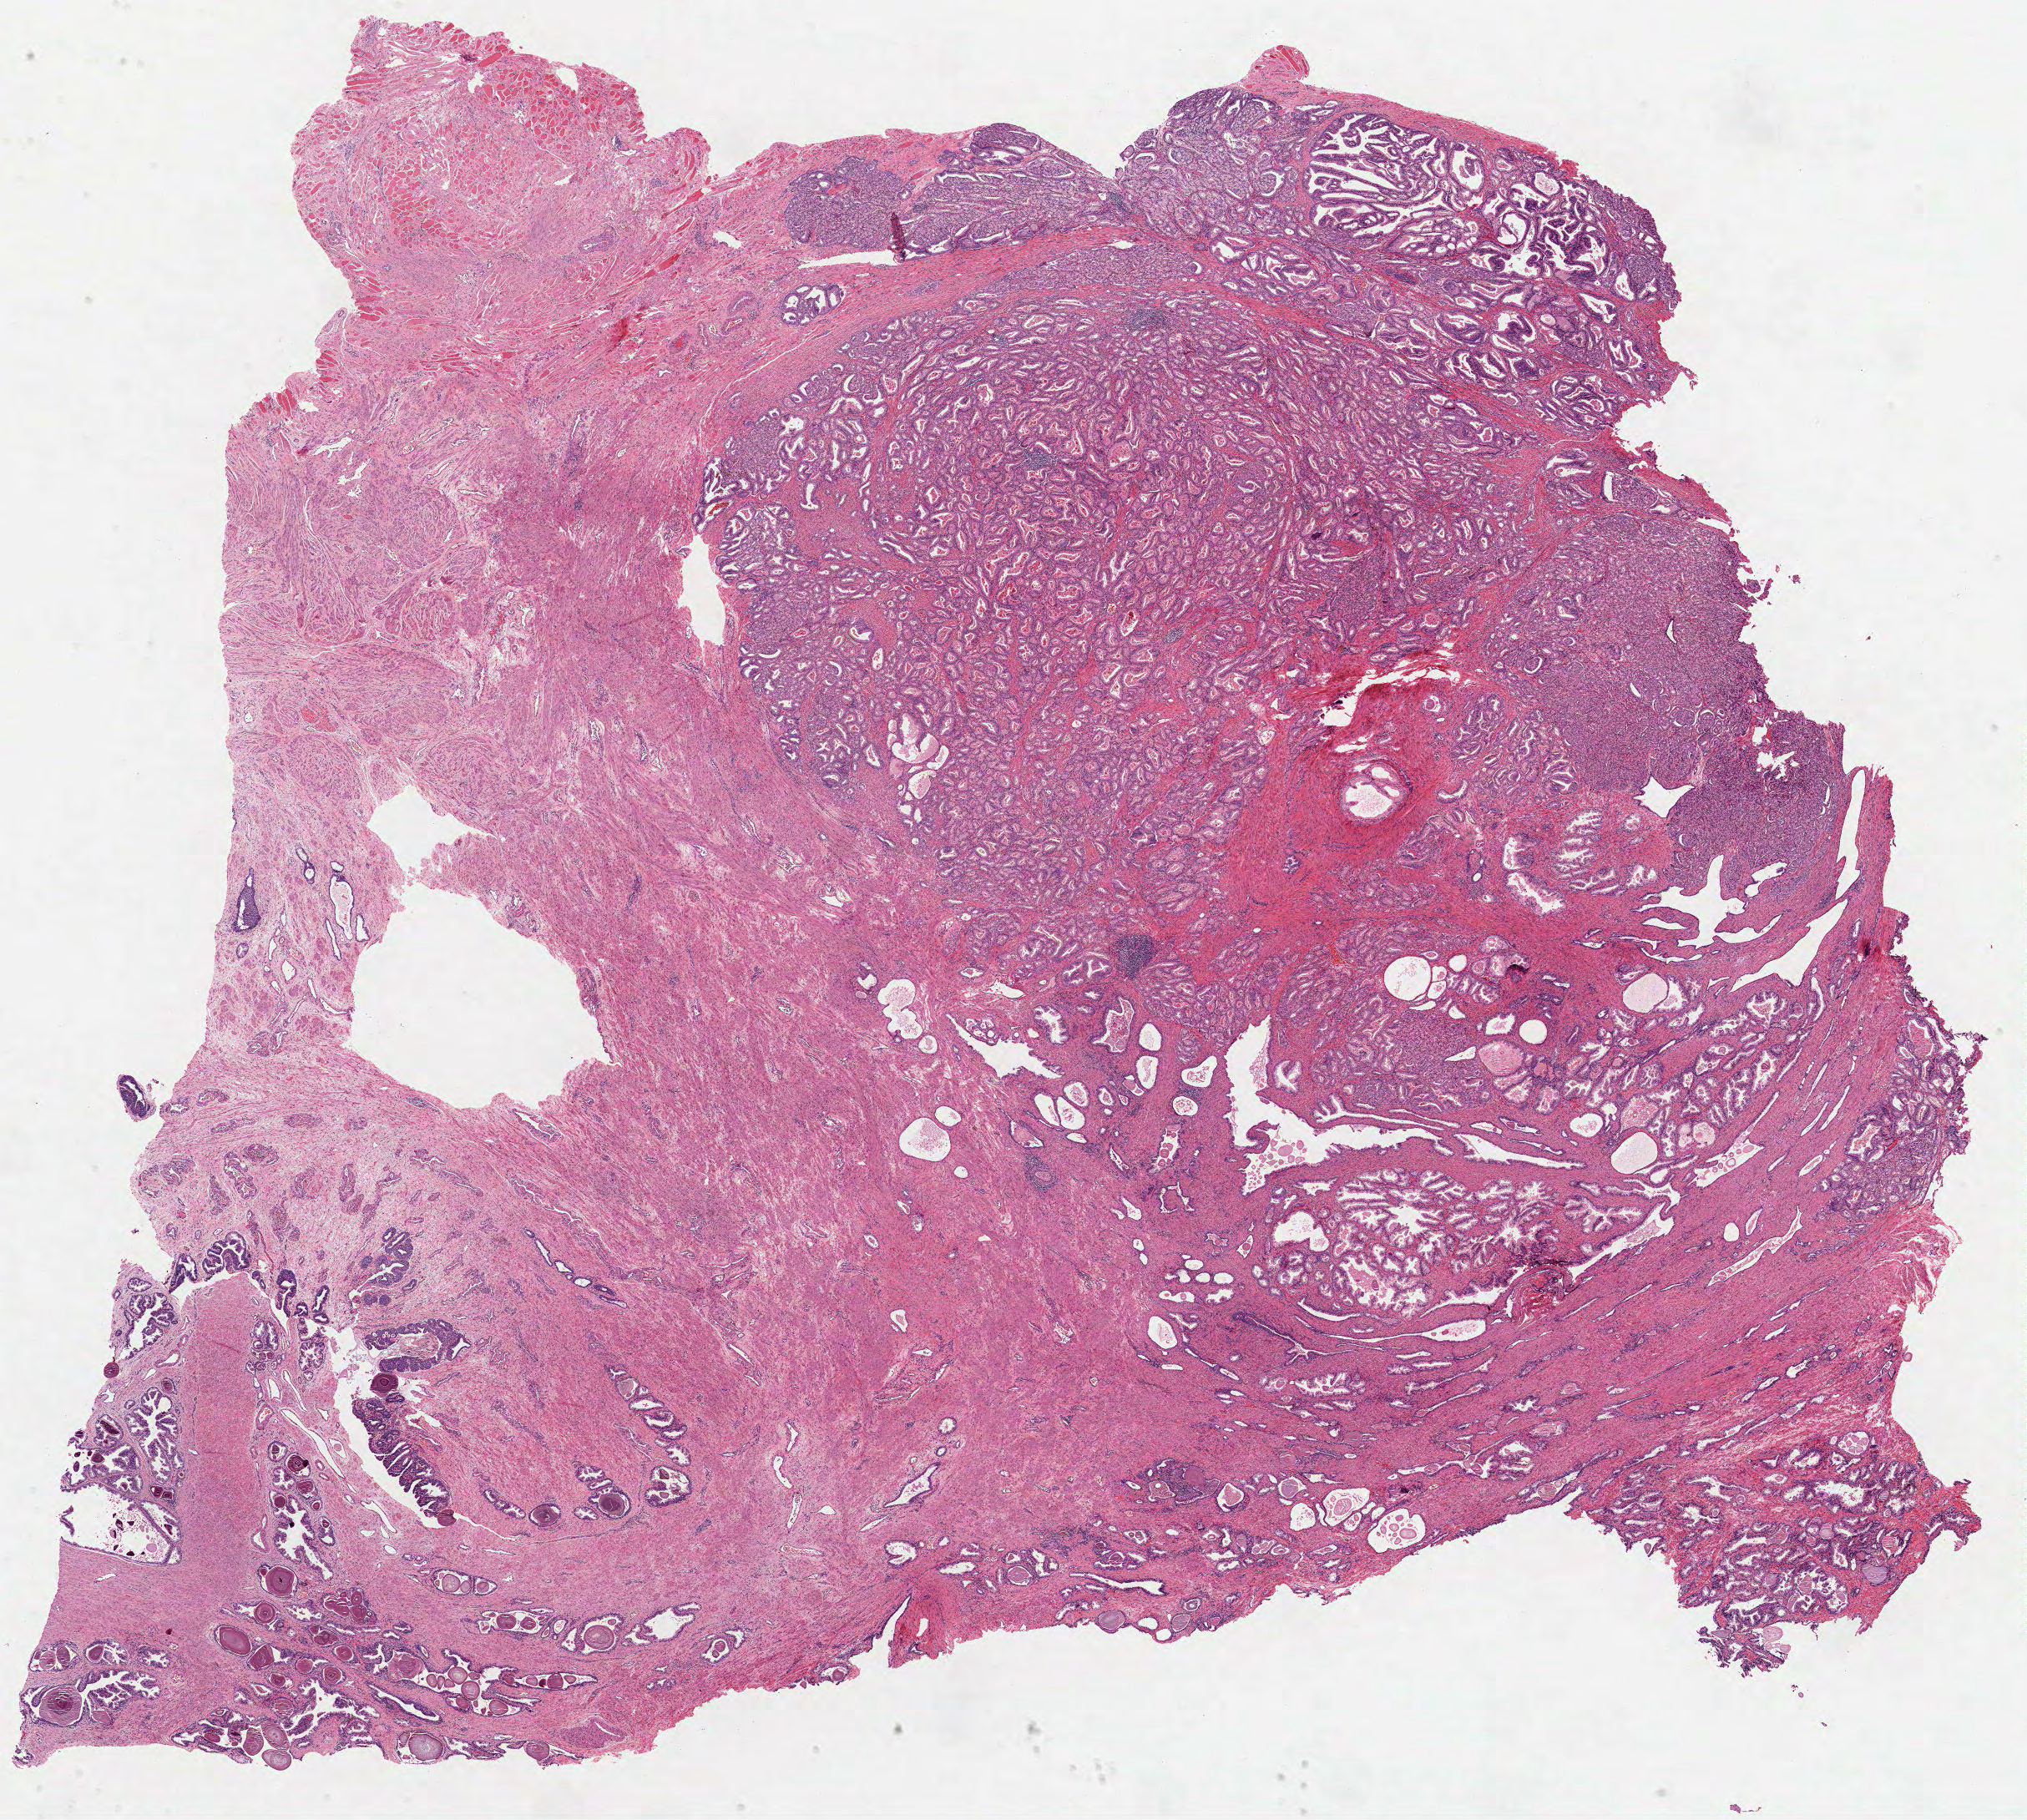
Digitized Hematoxylin and eosin (H&E) stained tissue section (whole slide) — low-resolution overview of the scanned area, about 19.6 x 17.6 mm (acquisition: 40x scan), formalin-fixed paraffin-embedded (FFPE) diagnostic section, prostate, primary tumour sample. Male patient; age at initial diagnosis 64 years. Gleason score: 7 (3+4).
Laterality: bilateral. Histologic diagnosis: Acinar cell carcinoma (prostate gland).